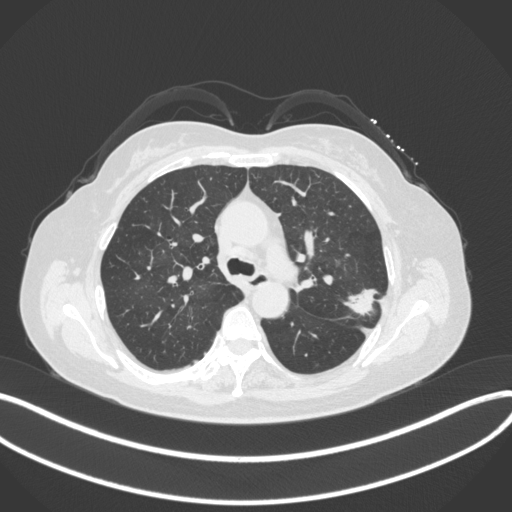
Chest CT, one axial slice. Lung window (W 1500 / L -600 HU). 1 mm slice thickness. 512 × 512 image matrix, field of view 400 × 400 mm. Patient: female, 60 years. Case-level facts recorded for this patient, not image findings: clinical TNM (as recorded): T1c N0 M0.
Structures marked on this image (rectangle marked by the reading radiologist):
- lung tumour (recorded histology: adenocarcinoma): box from (x=343, y=282) to (x=380, y=320) px